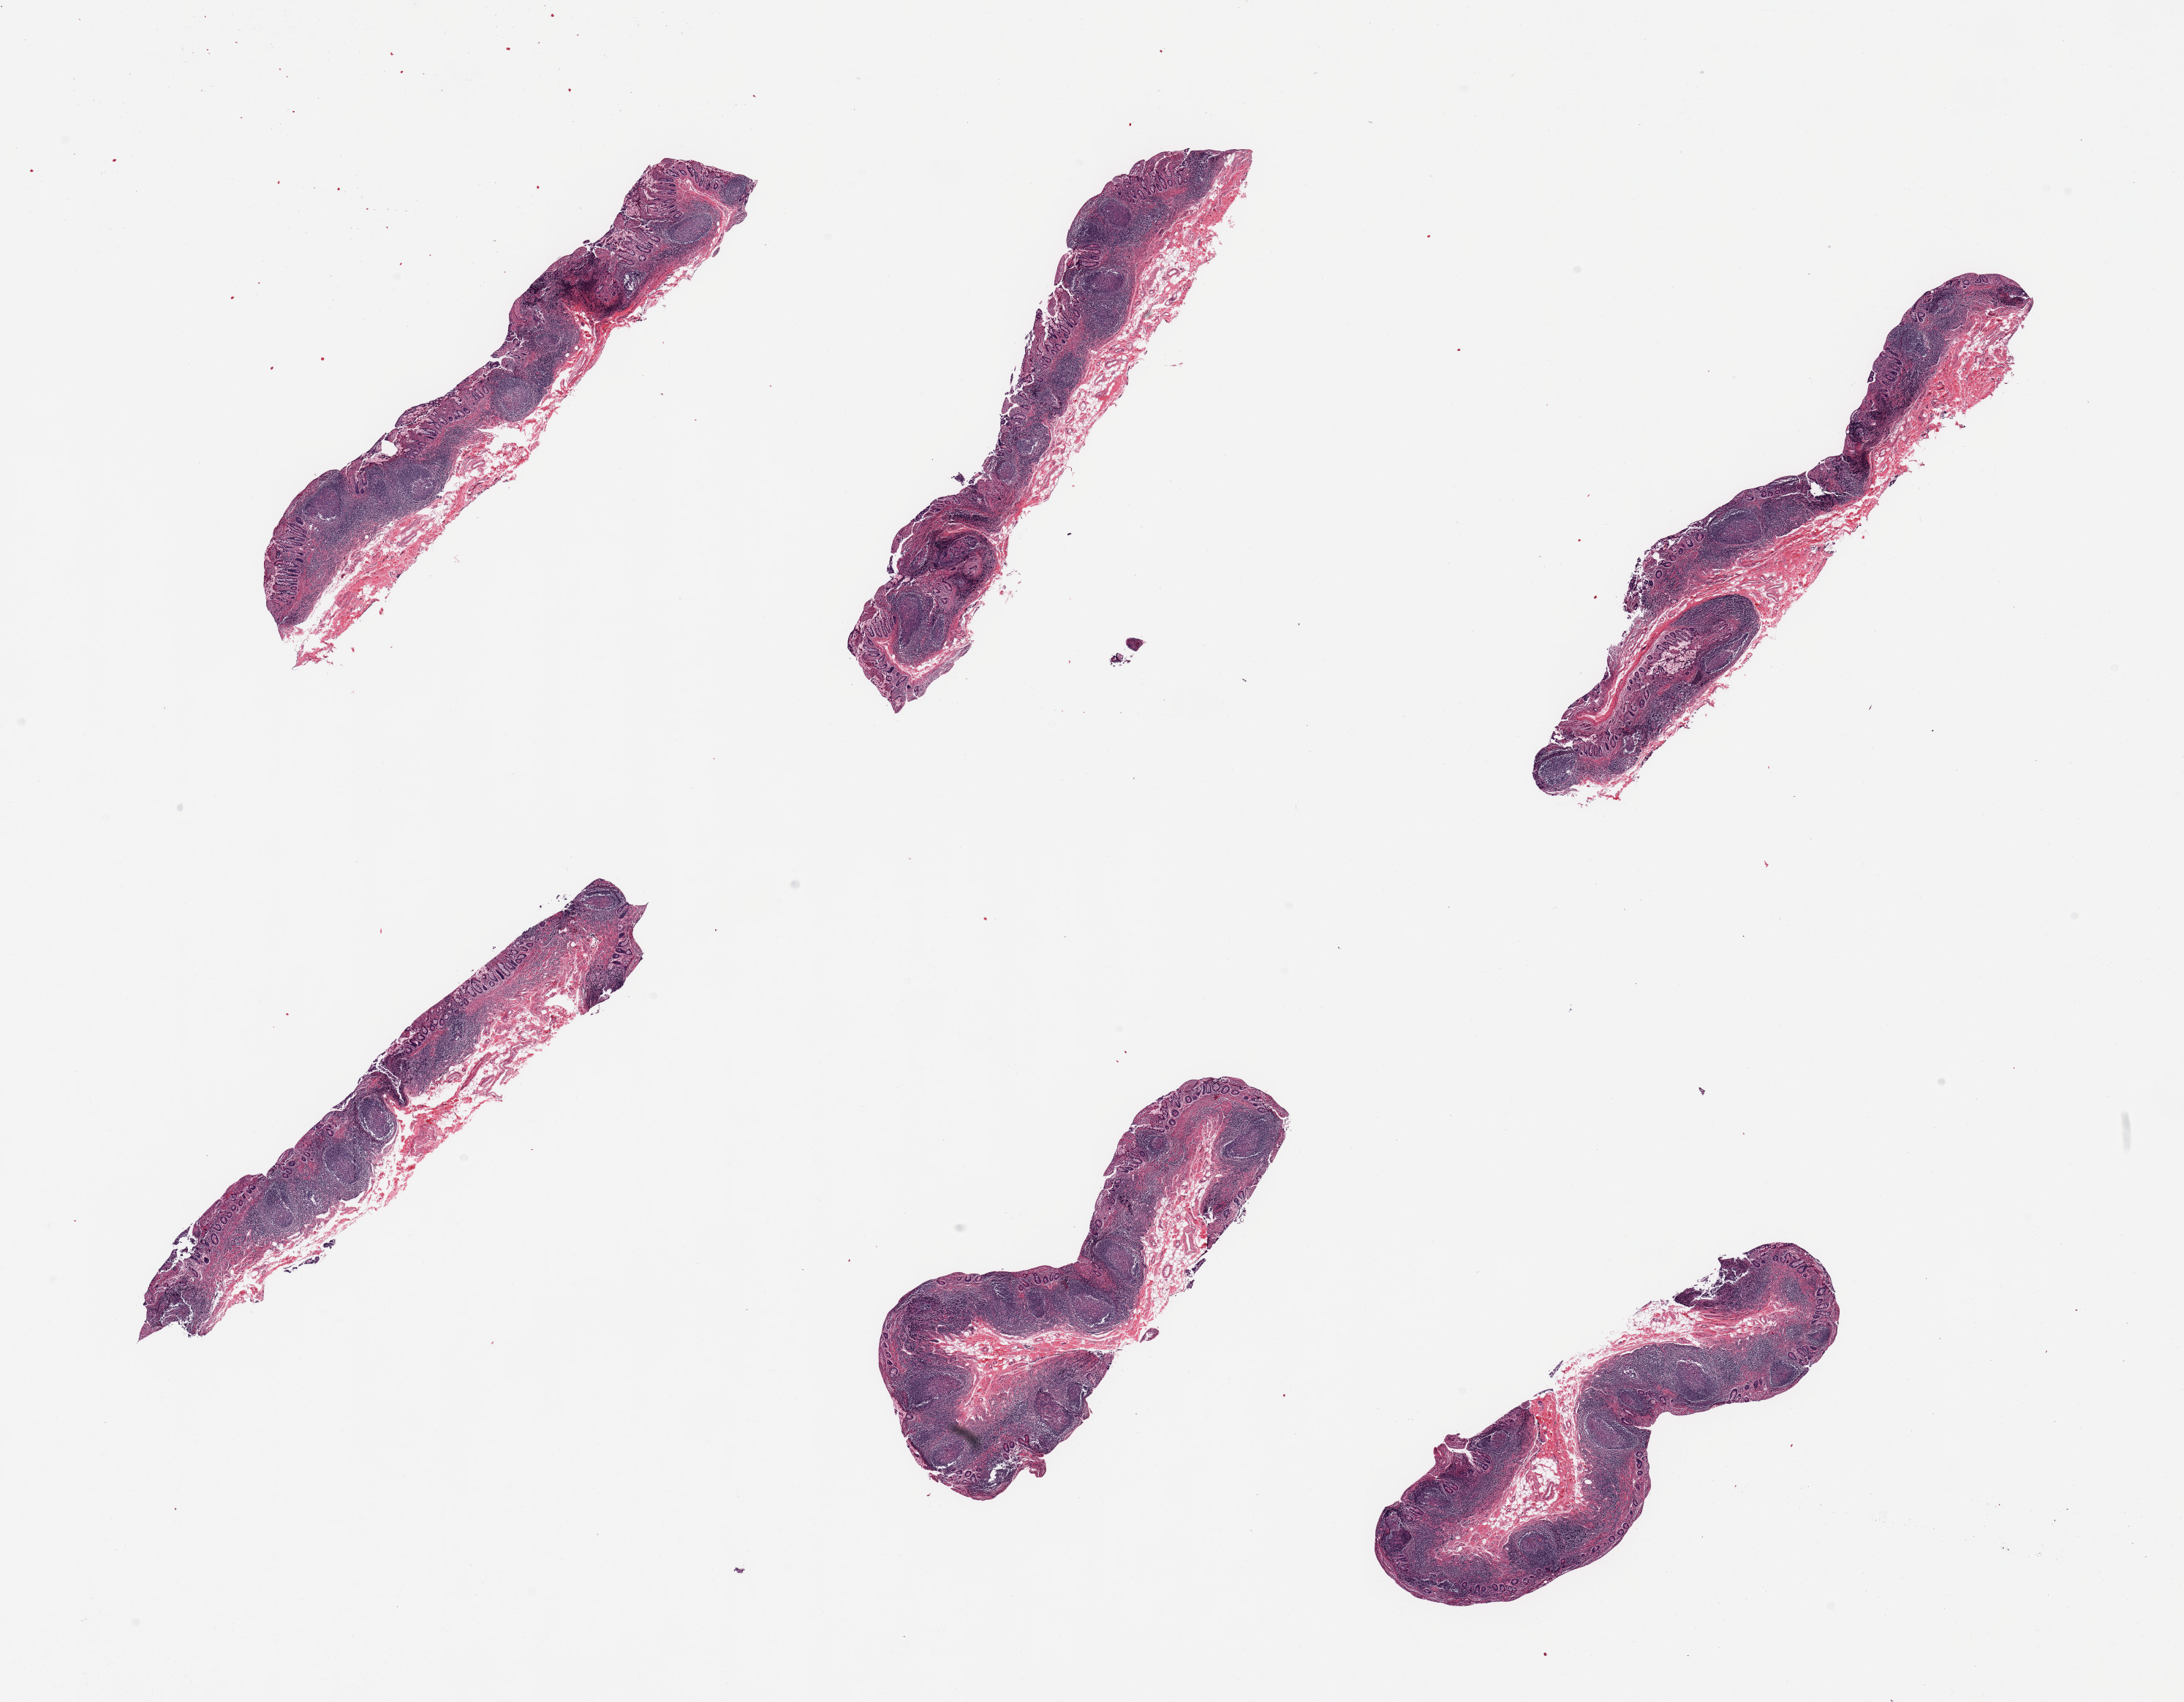
Digitized hematoxylin and eosin (H&E)-stained section, a low-resolution overview of the entire scanned area, about 23.6 x 18.4 mm (slide scanned at 20x); PAXgene-fixed, paraffin-embedded tissue; sampled site (target tissue): ileum; donor tissue sample. Donor: male.
• review note (as recorded): 6 pieces; good lymphoid component